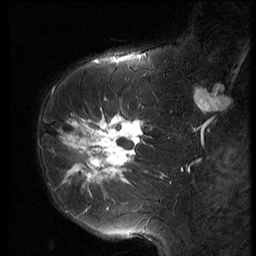
Breast MRI (dynamic contrast-enhanced), one sagittal slice. Position 22 of 56 along the scan axis. 3 images stored at this slice position (order not interpretable as contrast timing). 1.5 T. TE 4.2 ms, TR 9 ms. 2.5 mm slice thickness. 256 × 256 image matrix, field of view 180 × 180 mm. Patient: female, 61 years. Case-level facts recorded for this patient, not image findings: setting: breast cancer imaged before/during neoadjuvant chemotherapy; receptor status: HR-positive, HER2-negative.
Annotated regions visible in this slice (semi-automatic segmentation, software-assisted and operator-edited):
- analysis volume of interest (the breast-tissue region the enhancement analysis was run in; not a lesion): box from (x=47, y=89) to (x=153, y=191) px
- tumour enhancement mask (voxels above the 140 % enhancement threshold inside the analysis volume of interest): (x=61, y=115)–(x=144, y=191)